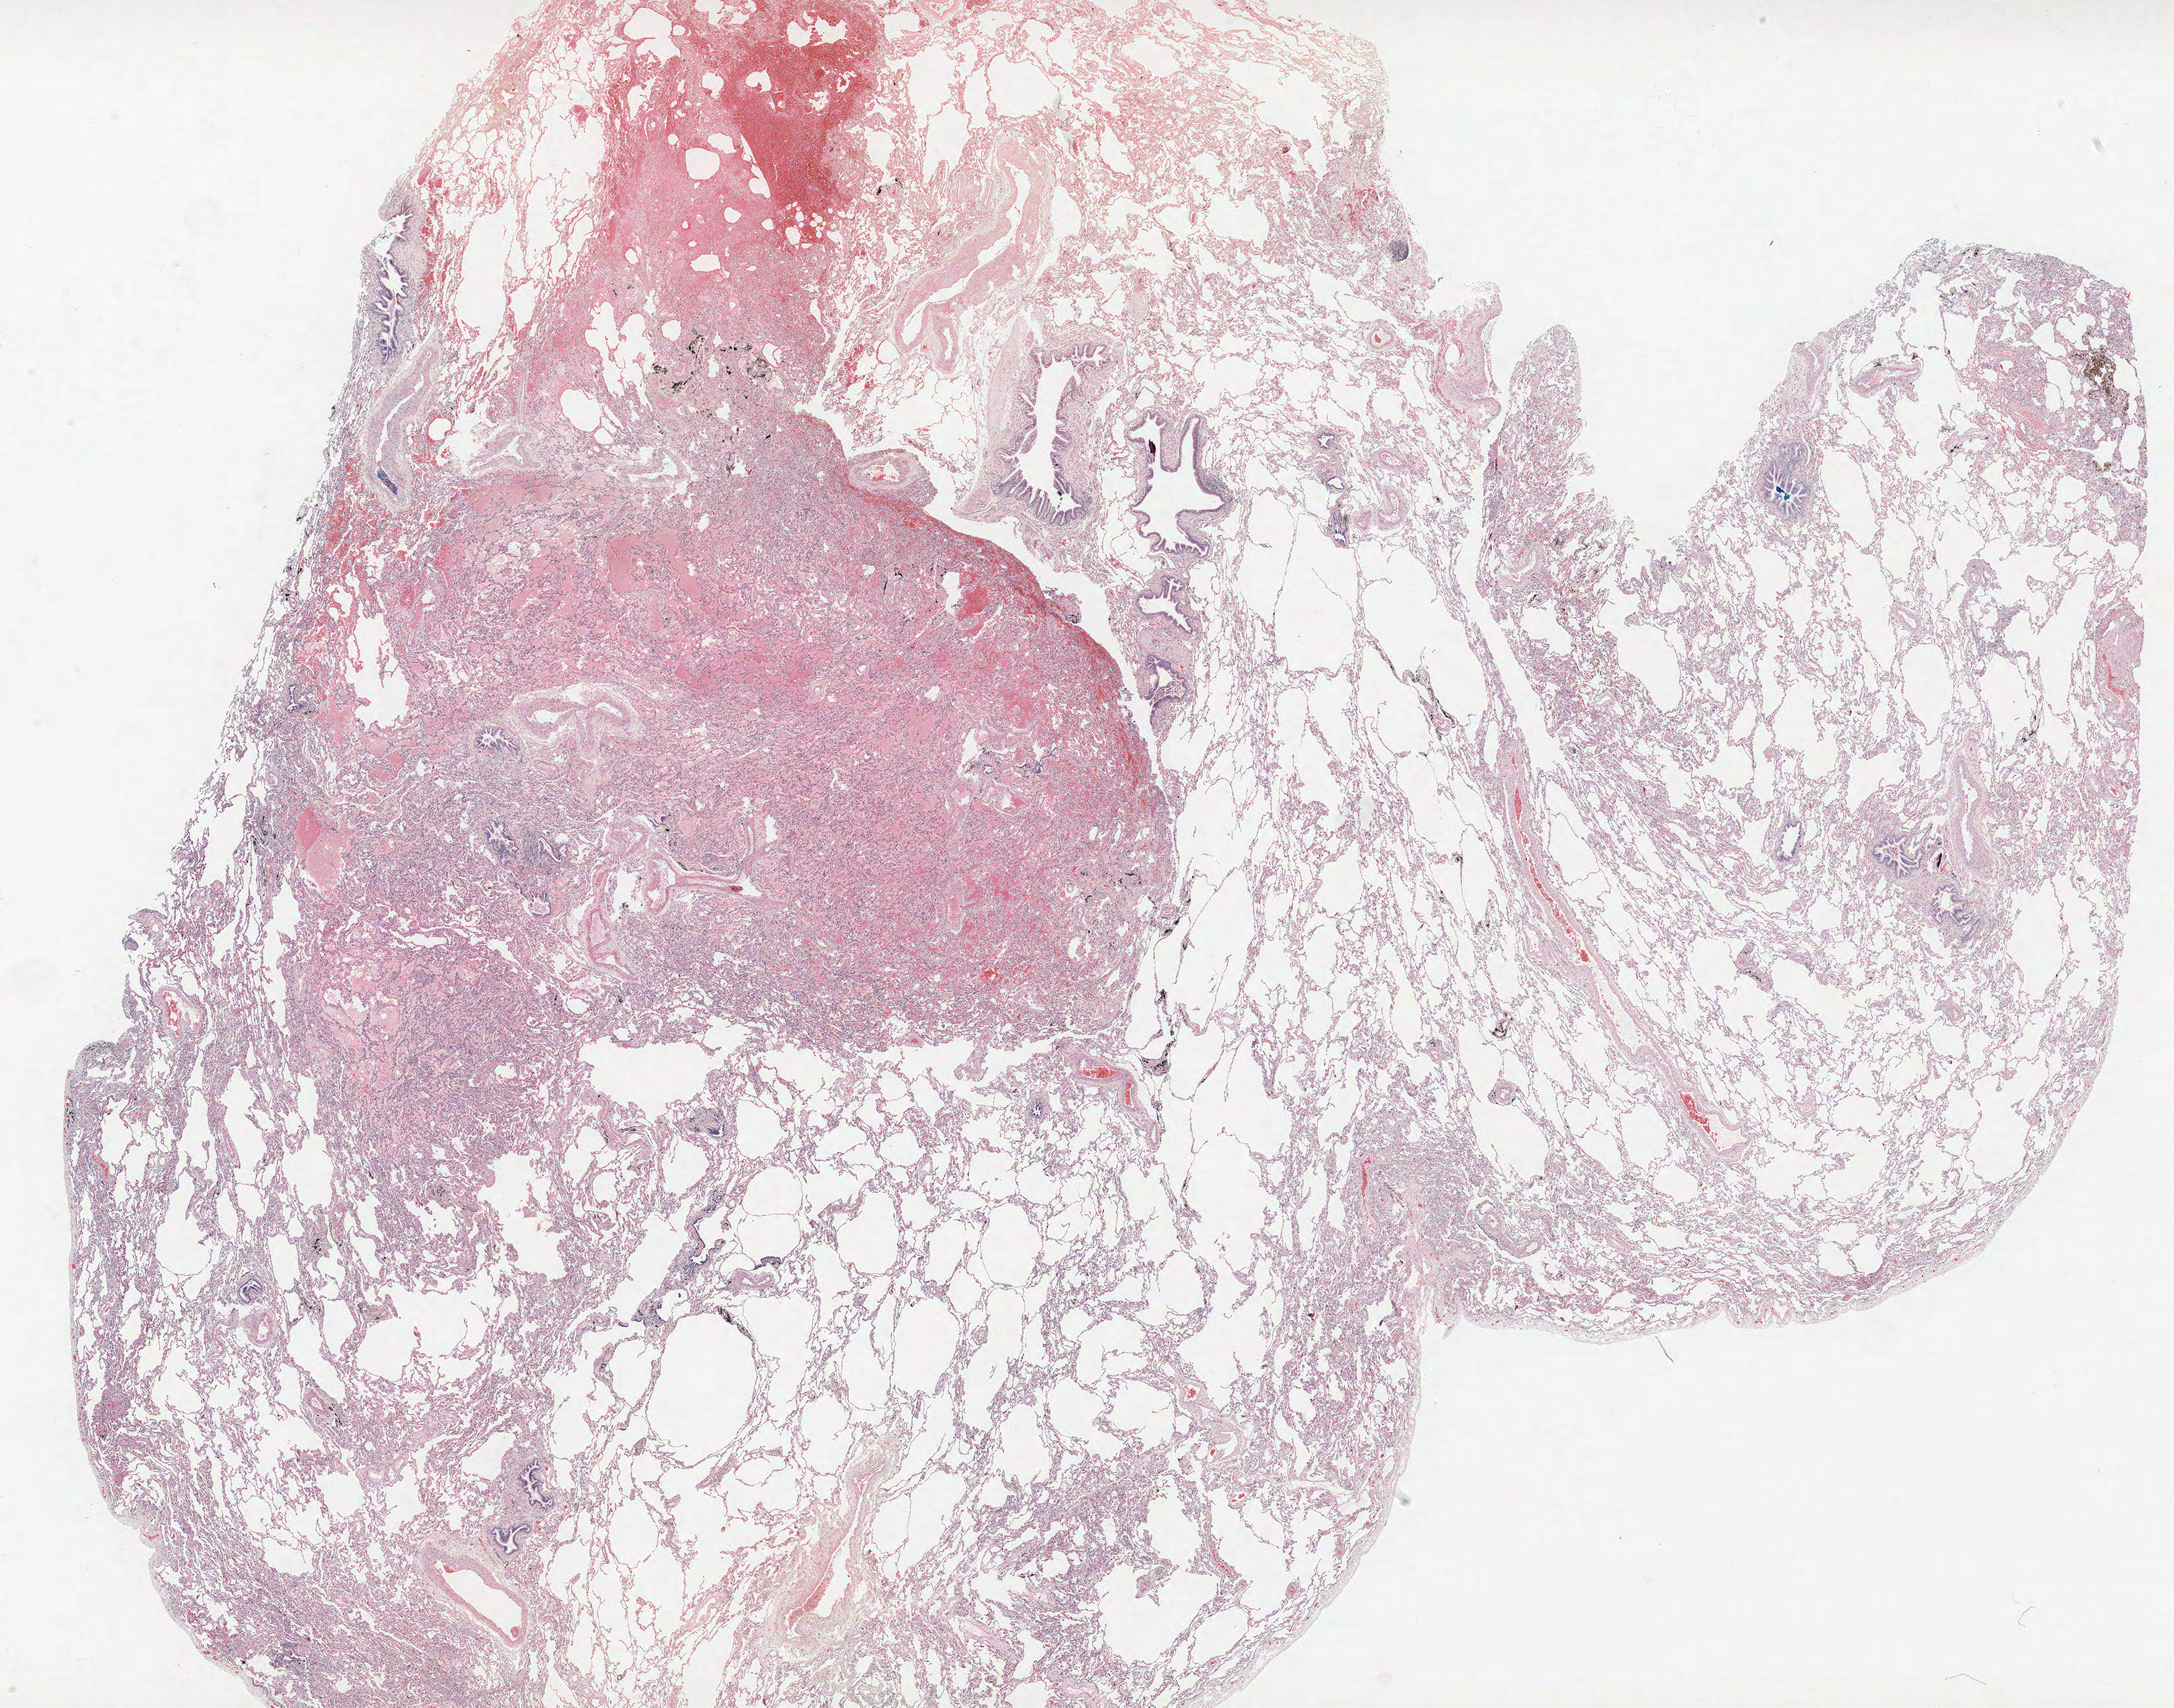
Whole-slide histology image, H&E, a low-resolution overview of the entire scanned area, about 26.6 x 20.9 mm (slide scanned at 40x), FFPE section, lung. Male, age 61 at enrolment. Former smoker at enrolment. Grade: moderately differentiated (G2).
* tumour size (pathology): 30 mm
* primary tumour location (clinical record): right lower lobe
* stage (AJCC 6th edition): IA
* participant's lung-cancer diagnosis: Adenocarcinoma, NOS (ICD-O-3 8140/3)